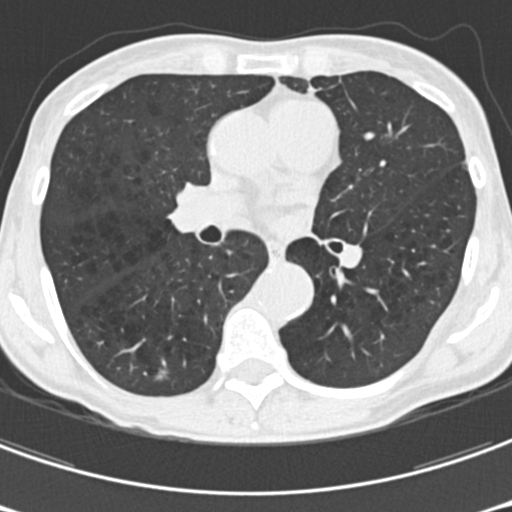
Low-dose screening chest CT, one axial slice. Position 96 of 176 along the scan axis. Reconstruction kernel B30f. 120 kVp. Lung window (W 1500 / L -600 HU). 512 × 512 image matrix, field of view 277 × 277 mm.
Structures marked on this image (expert manual segmentation):
- lesion 2 (nodule, upper lobe of right lung): bounding box [x1, y1, x2, y2] px = [156, 370, 167, 381]